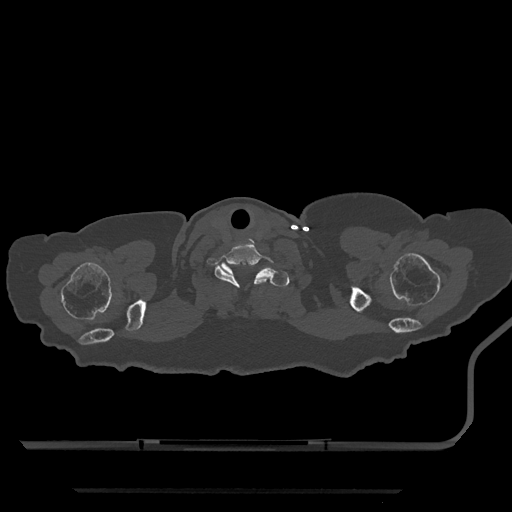
CT including the spine, one axial slice; reconstruction kernel Br40s/3; 120 kVp; bone window (W 1800 / L 400 HU); 0.5 mm slice thickness; 512 × 512 image matrix, field of view 440 × 440 mm. Patient: female, 51 years. From the clinical record (not read from this slice): primary cancer: neuro; vertebrae with lytic lesions (as recorded): T8.
Structures marked on this image (semi-automatically segmented with operator editing):
- T1 vertebra: bounding box <221,263,290,287> (left, top, right, bottom; pixels)